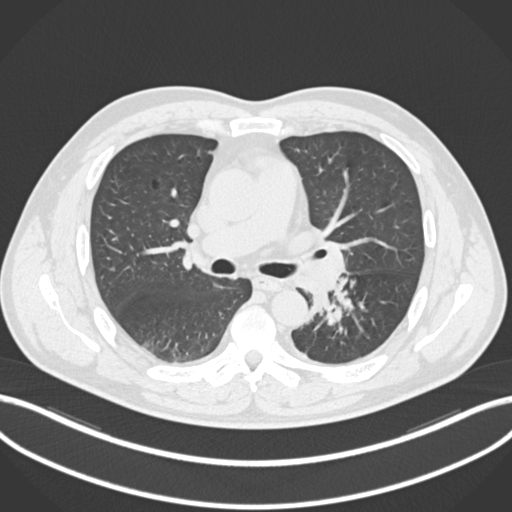
Chest CT, one axial slice. Position 135 of 223 along the scan axis. Reconstruction kernel B30f. 120 kVp. Lung window (W 1500 / L -600 HU). 512 × 512 image matrix, field of view 400 × 400 mm. Male patient, age 50 years. From the clinical record (not read from this slice): clinical TNM (as recorded): T2a N3 M0.
Annotated regions visible in this slice (rectangle marked by the reading radiologist):
- lung tumour (recorded histology: squamous cell carcinoma): box from (x=306, y=277) to (x=357, y=329) px